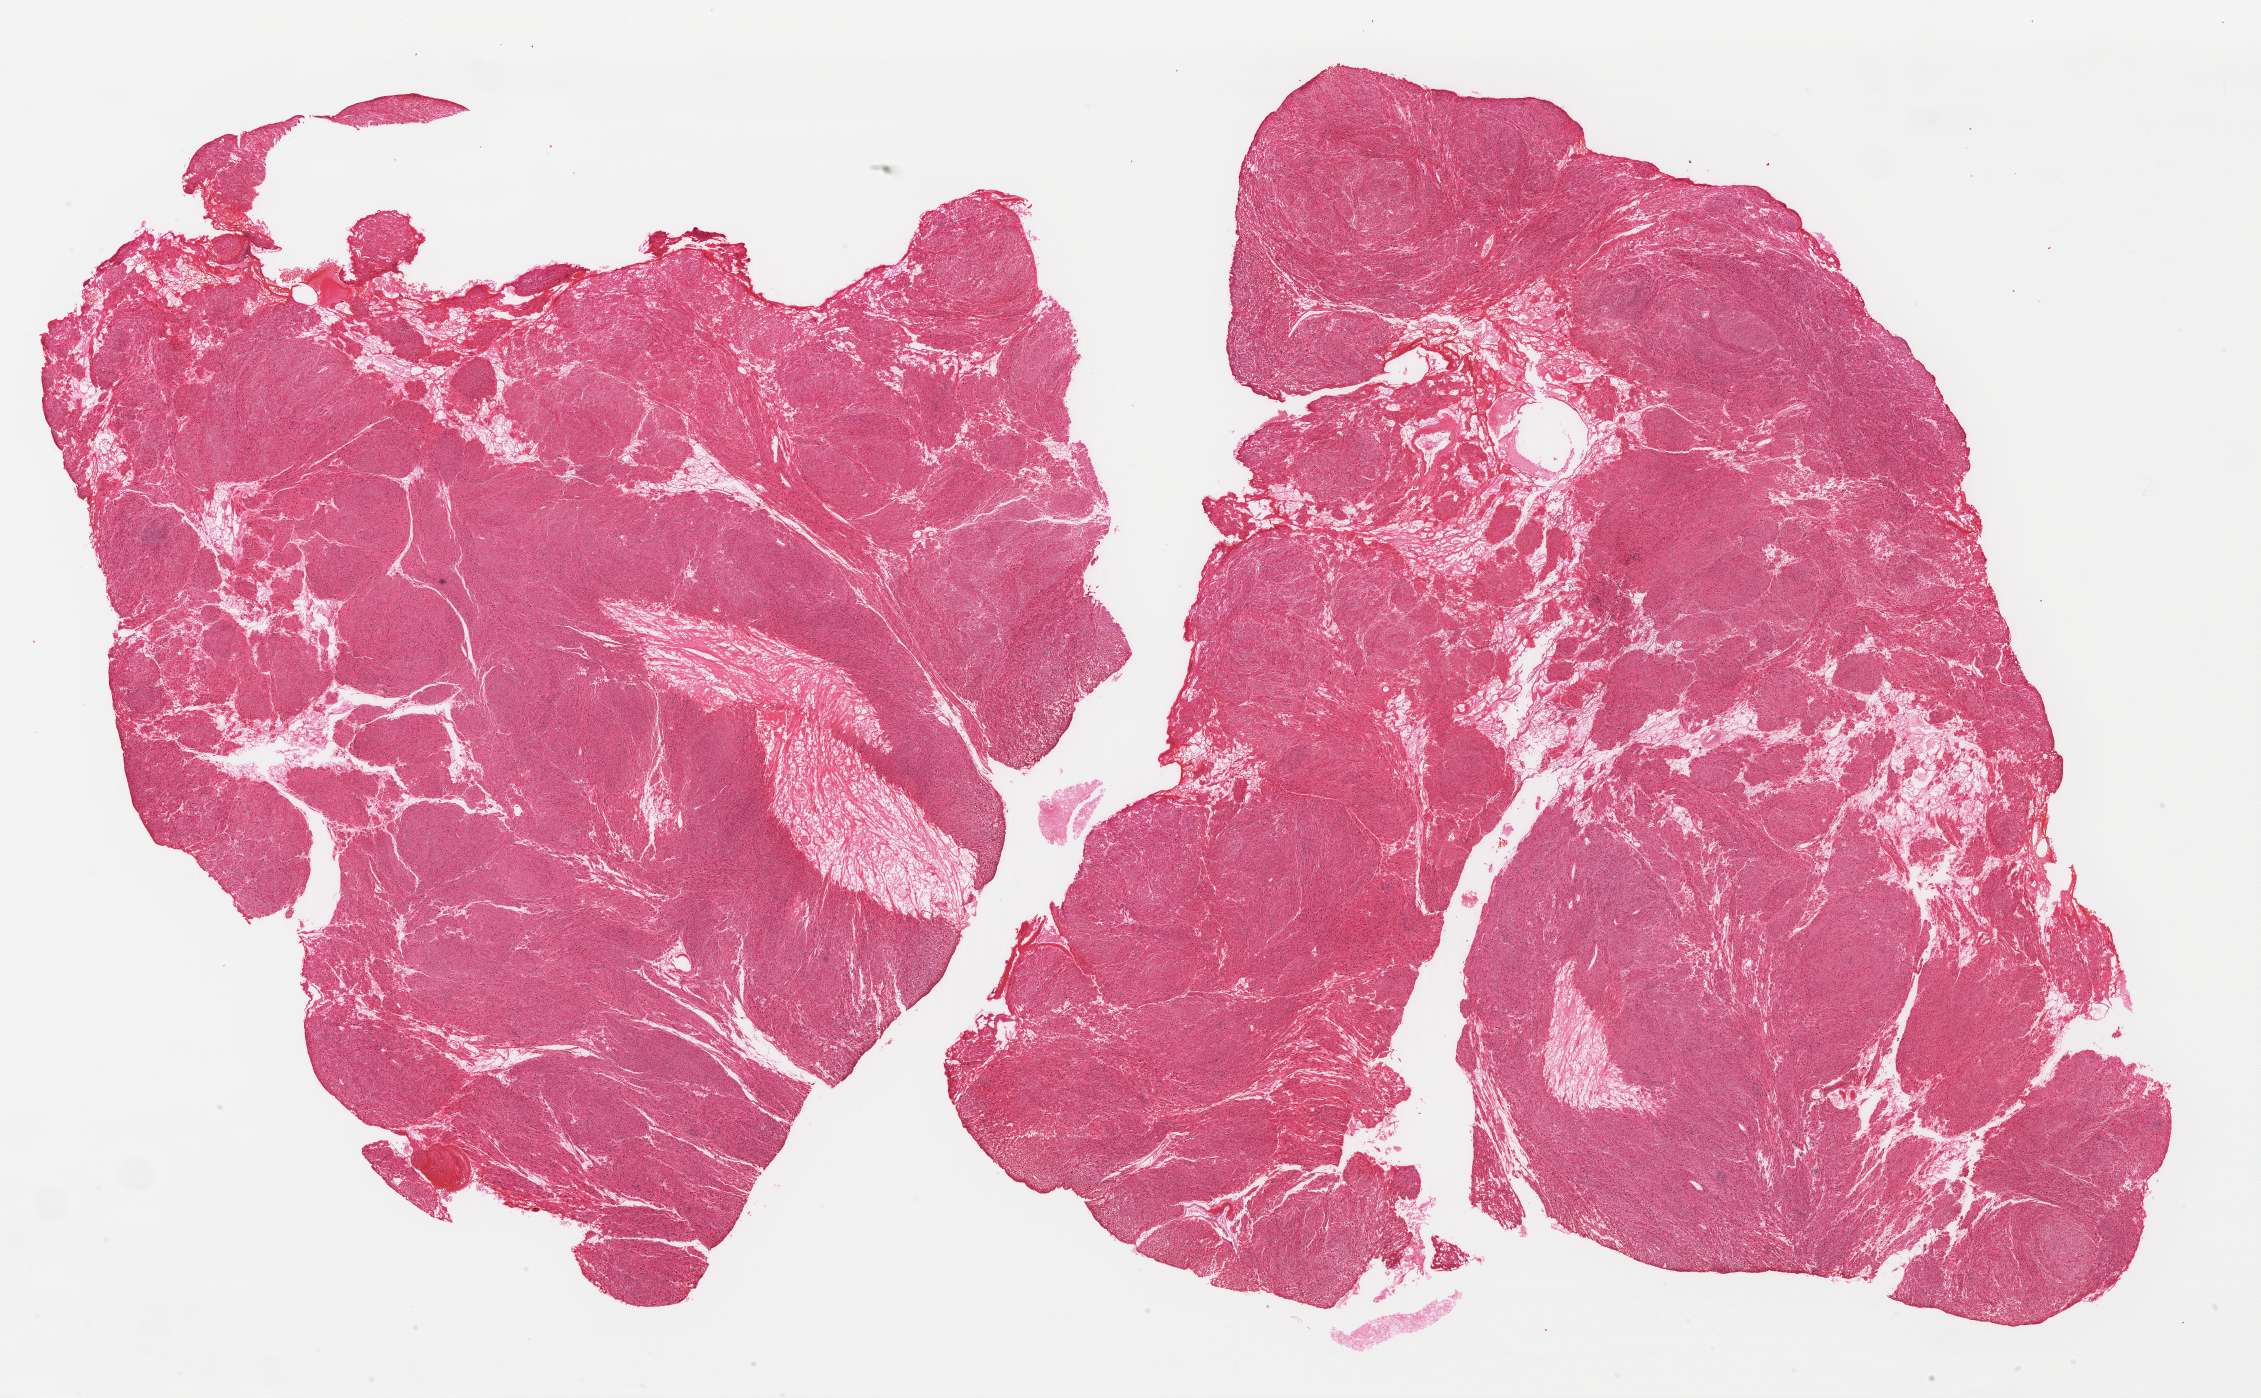
H&E-stained whole-slide image — whole scanned area (about 35.5 x 22.0 mm) shown as a low-resolution overview. Formalin-fixed paraffin-embedded (FFPE) diagnostic section. Retroperitoneum and peritoneum, primary tumour sample. Patient: male, age at initial diagnosis 67 years.
Pathologic diagnosis: Leiomyosarcoma, NOS (retroperitoneum).